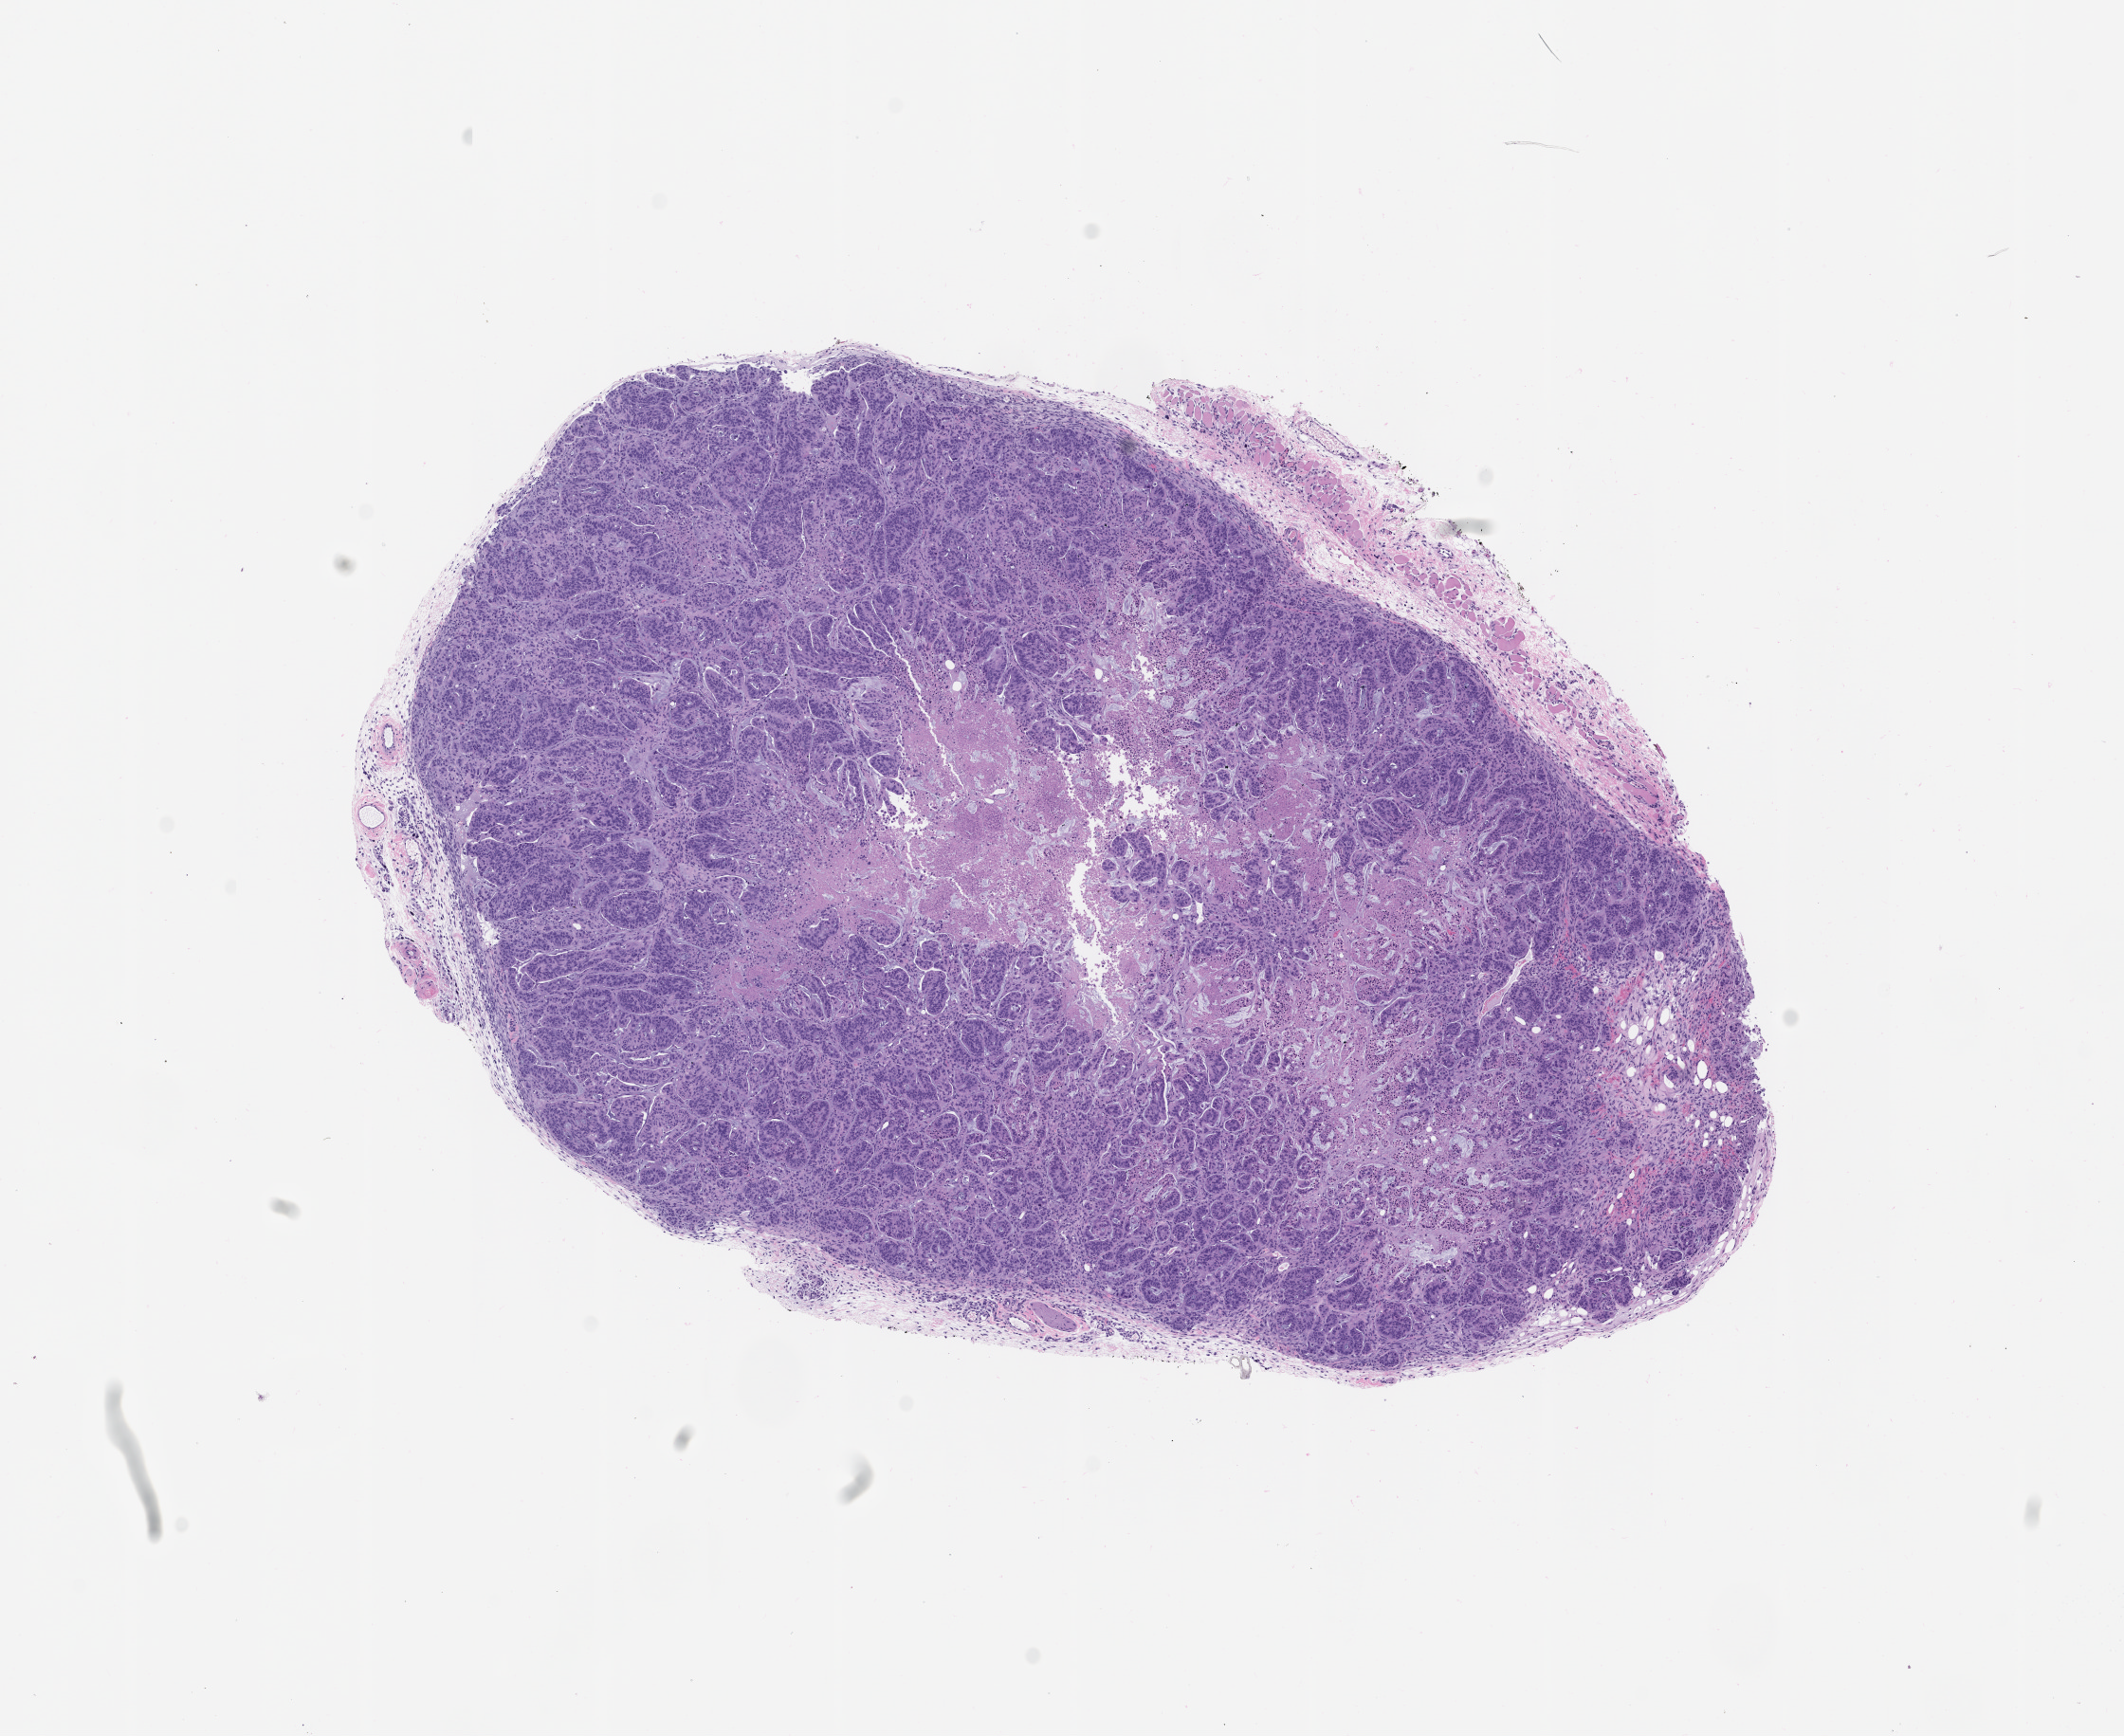
Whole-slide image, hematoxylin and eosin (H&E): patient-derived xenograft (human tumor grown in a mouse), passage 0 — a low-resolution overview of the entire scanned area, about 9.0 x 7.3 mm, formalin-fixed, paraffin-embedded (FFPE) tissue, originating tumor site category: small intestine.
Originating patient diagnosis: Small Intestinal Adenocarcinoma.